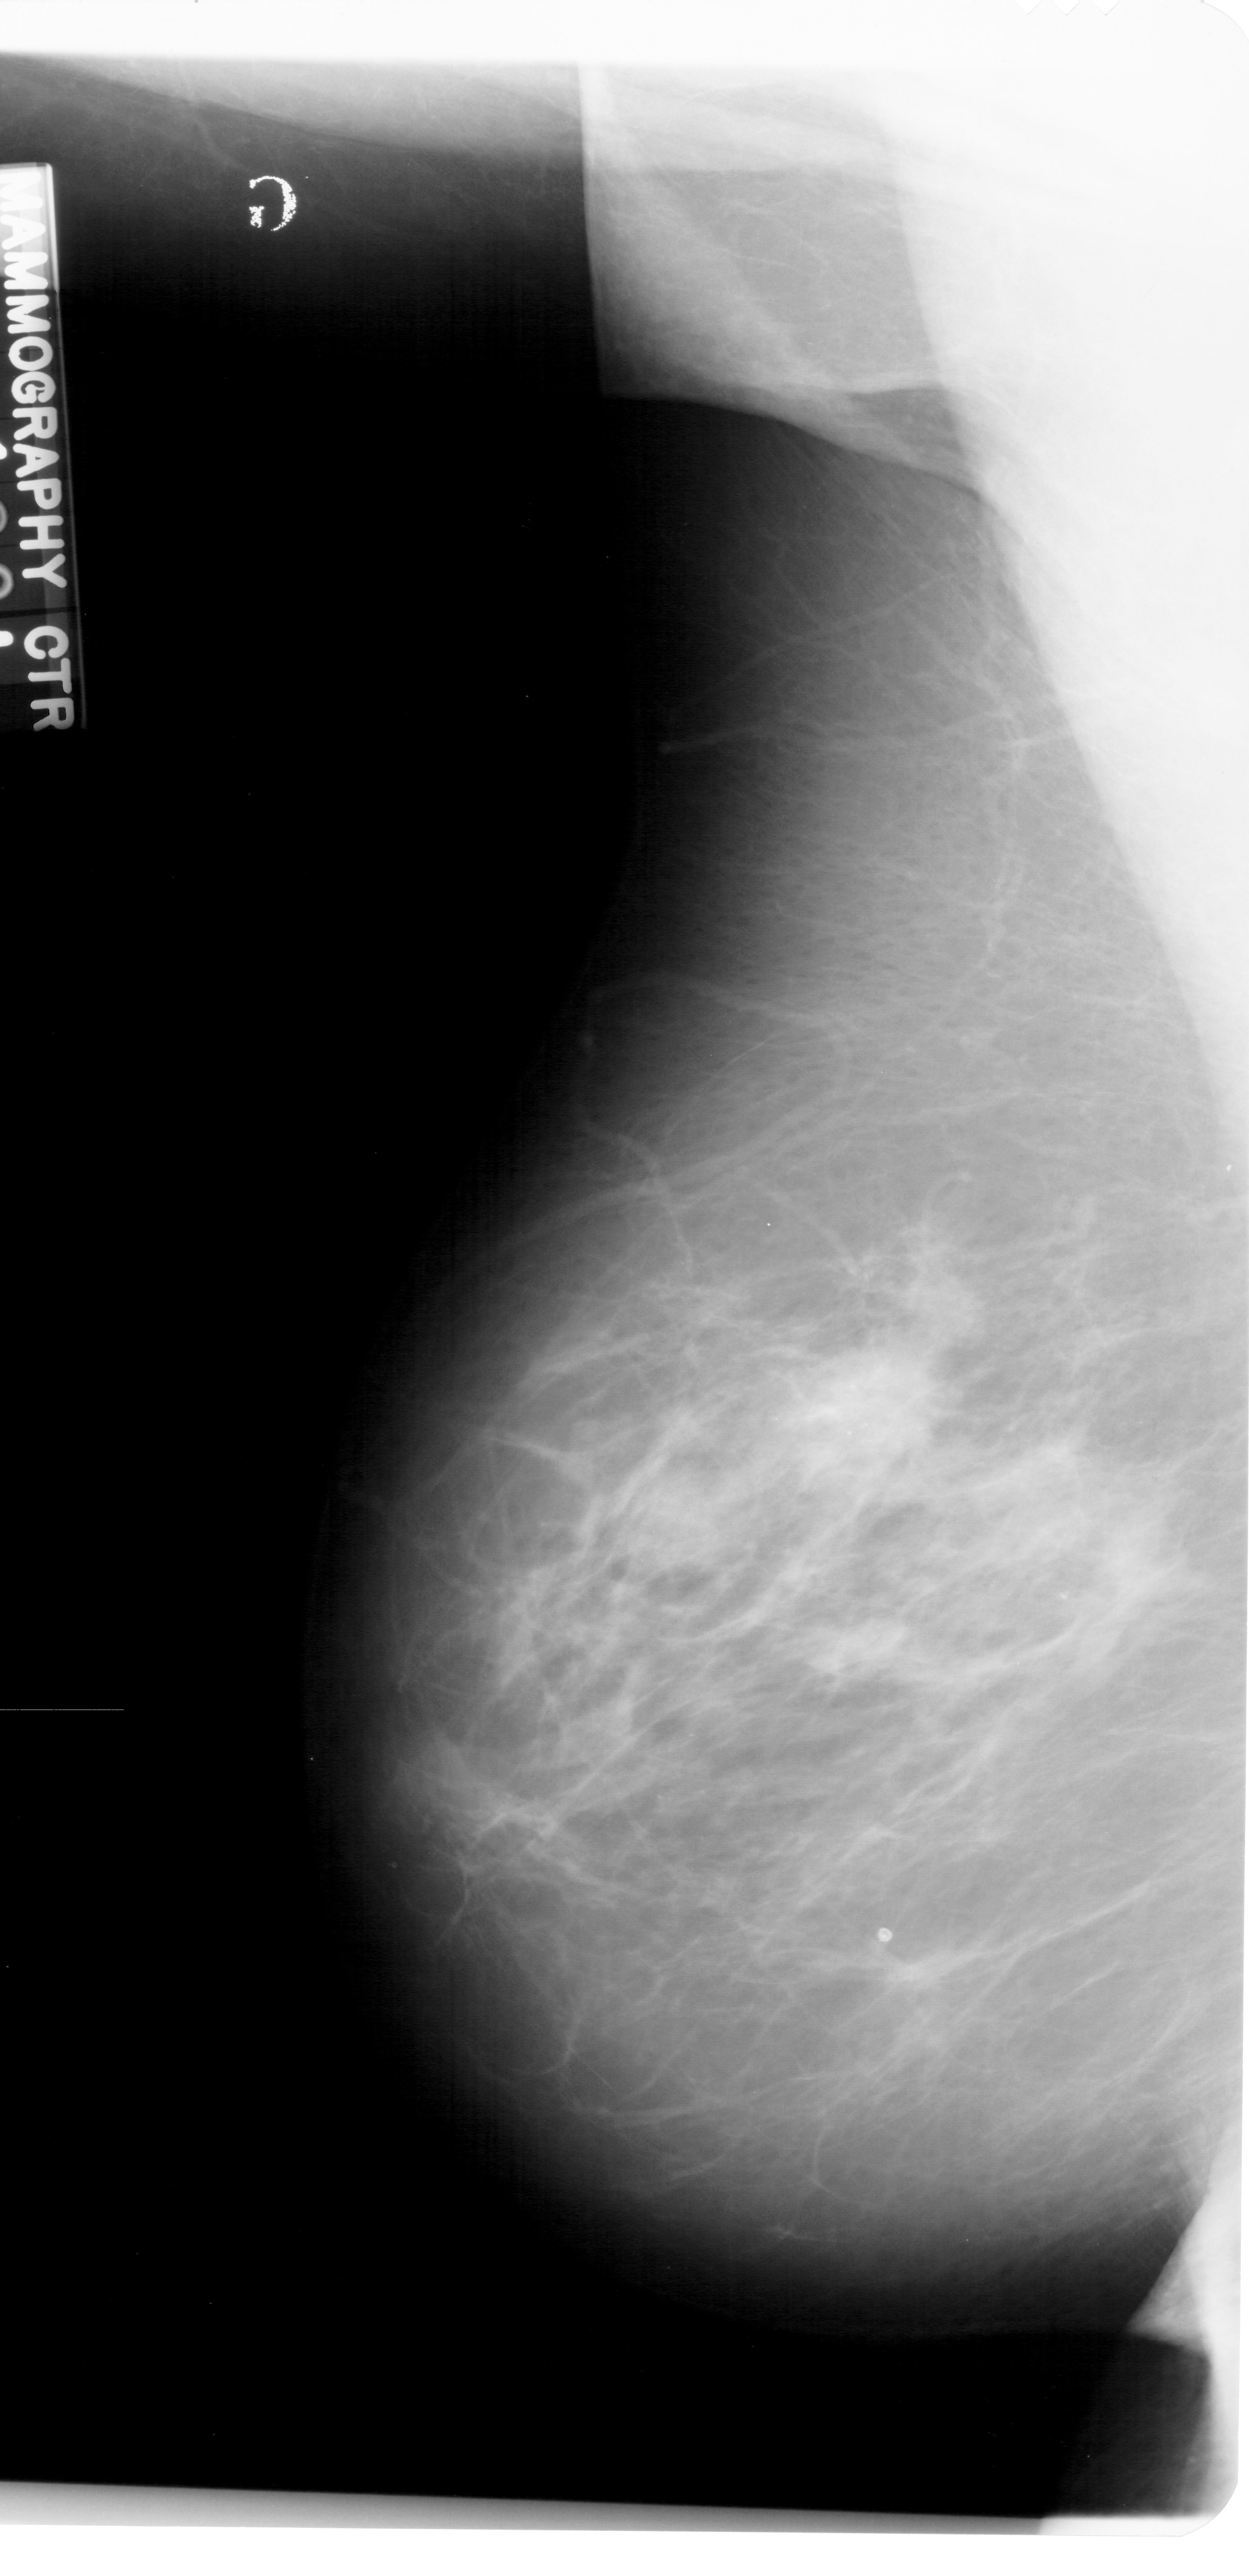
Mammogram (digitized film), left breast, mediolateral oblique (MLO) view, BI-RADS breast density category 3 (scale 1–4).
Finding: mass, shape irregular, margins spiculated; BI-RADS assessment category 5; pathology result (as recorded, not read from the image): malignant.